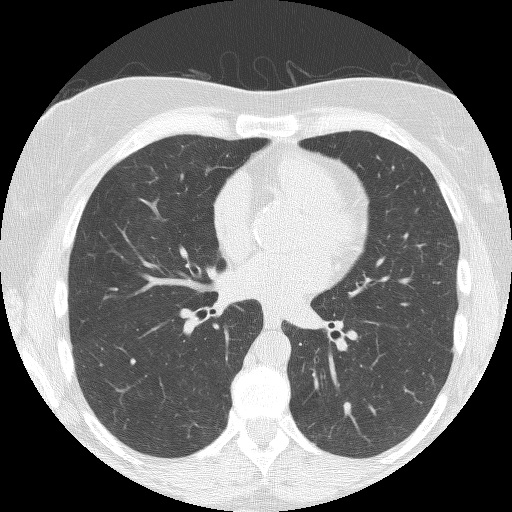
Axial slice from a low-dose chest CT screening exam, second screening round (one year after baseline), lung window (W 1500 / L -600 HU), 2.5 mm slice thickness, 120 kVp, slice 75 of 150 in the series. Female, age 60 years at enrolment.
Expert reader's lesion annotation, bounding box <323,384,359,426> (left, top, right, bottom; pixels). Reader record for this screening exam (exam-level; its link to the box is not recorded): non-calcified nodule or mass ≥4 mm, left lower lobe, 16 × 7 mm, smooth margins, soft tissue attenuation, pre-existing on the prior screen: no. Lung cancer was diagnosed 54 days after this screen: small cell carcinoma, NOS, left lower lobe, stage IIA (AJCC 6th edition), 12 mm at pathology.